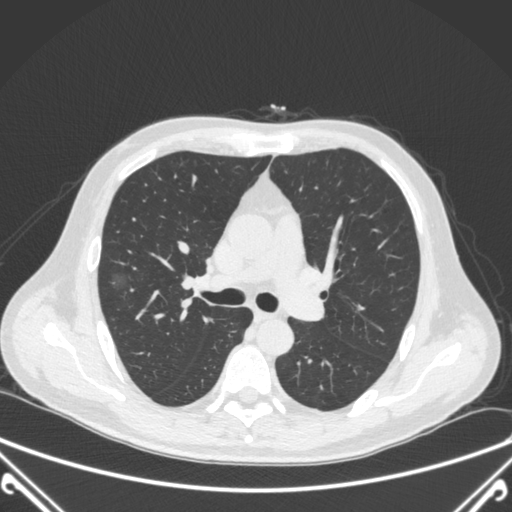
Chest CT, one axial slice. Slice 230 of 360 in the series (ordered by position). 120 kVp. Lung window (W 1500 / L -600 HU). 1 mm slice thickness. 512 × 512 image matrix. Patient: male, 64 years. From the clinical record (not read from this slice): clinical TNM (as recorded): T1c N0 M0; histopathological grade: G2.
Structures marked on this image (bounding box drawn by a radiologist):
- lung tumour (recorded histology: adenocarcinoma): bounding box <104,264,141,297> (left, top, right, bottom; pixels)